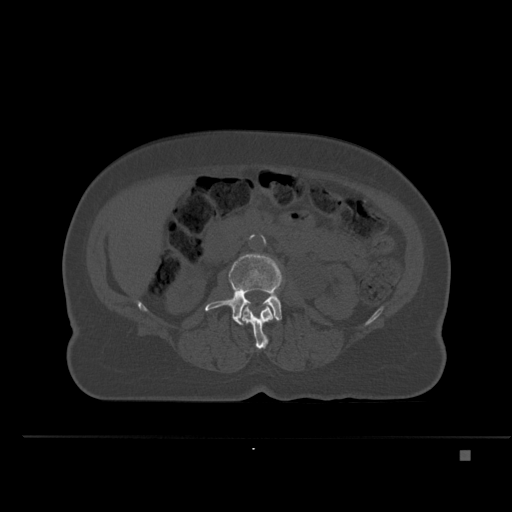
CT including the spine, one axial slice. Position 205 of 477 along the scan axis. Bone window (W 1800 / L 400 HU). 1.5 mm slice thickness. 512 × 512 image matrix, field of view 422 × 422 mm. Patient: female, 74 years. Case-level facts recorded for this patient, not image findings: primary cancer: colon.
Annotated regions visible in this slice (semi-automatic segmentation, software-assisted and operator-edited):
- L2 vertebra: bounding box <242,305,274,349> (left, top, right, bottom; pixels)
- L3 vertebra: <205,253,282,326>